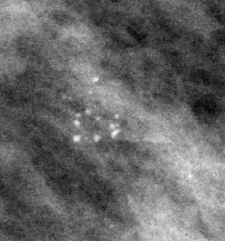
Region of interest cut from a scanned film mammogram (one marked finding), left breast, MLO view, BI-RADS breast density category 2 (scale 1–4).
- Calcifications, morphology punctate / pleomorphic, distribution clustered; BI-RADS assessment category 4; pathology (as recorded): malignant.